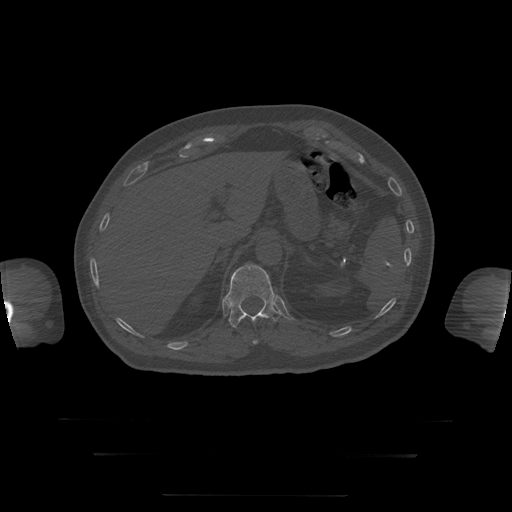
CT including the spine, one axial slice. Position 79 of 397 along the scan axis. Bone window (W 1800 / L 400 HU). 512 × 512 image matrix. Patient age 73 years. Case-level facts recorded for this patient, not image findings: primary cancer: prostate.
Outlined on this slice (semi-automatically segmented with operator editing):
- T11 vertebra: bounding box <253,340,258,345> (left, top, right, bottom; pixels)
- T12 vertebra: <228,265,281,329>